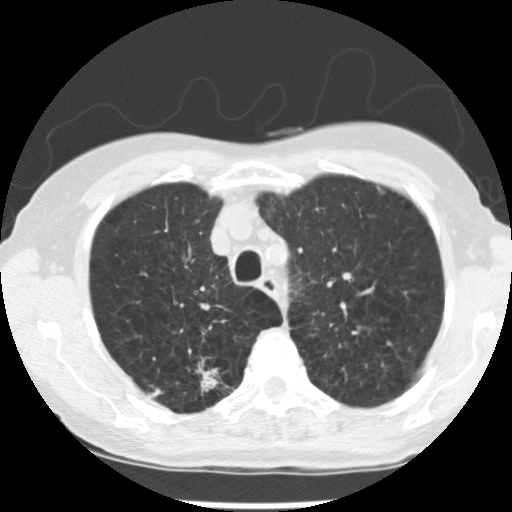
Low-dose screening chest CT, axial slice. Baseline screening round. Lung window (W 1500 / L -600 HU). 2.5 mm slice thickness. Standard (soft-tissue) reconstruction kernel (STANDARD). Slice 54 of 265 in the series. 512 × 512 image matrix. Female, age 72 years at enrolment.
Expert reader's lesion annotation, bounding box [x1, y1, x2, y2] px = [183, 355, 237, 406]. The screening reader recorded 3 non-calcified nodules or masses ≥4 mm on this exam (right upper lobe, left upper lobe, left lower lobe); which of them this box marks is not recorded. Participant outcome: lung cancer diagnosed 50 days after this screen — adenocarcinoma, NOS, right upper lobe, moderately differentiated (G2), stage IB (AJCC 6th edition), 22 mm at pathology.